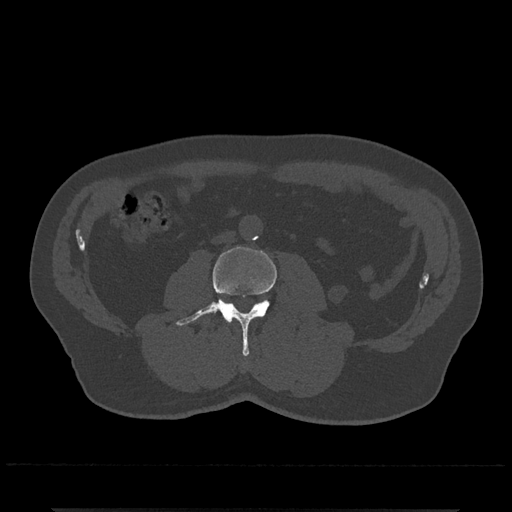
CT including the spine, one axial slice. 120 kVp. Bone window (W 1800 / L 400 HU). 512 × 512 image matrix, field of view 393 × 393 mm. Patient: male, 67 years. From the clinical record (not read from this slice): primary cancer: prostate.
Structures marked on this image (semi-automatic segmentation, software-assisted and operator-edited):
- L3 vertebra: box from (x=176, y=247) to (x=277, y=356) px